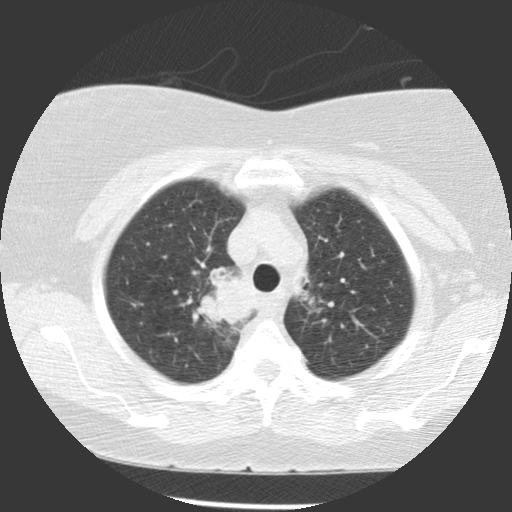
Low-dose screening chest CT, axial slice. First (baseline) screen. Lung window (W 1500 / L -600 HU). 2.5 mm slice thickness. Slice 91 of 116 in the series. 512 × 512 image matrix, field of view 320 × 320 mm. Female participant, aged 63 years at enrolment.
• Expert-annotated lung lesion, box from (x=200, y=266) to (x=258, y=328) px.
• Screening reader's record for this exam (one nodule recorded; not confirmed to be the boxed lesion): non-calcified nodule or mass ≥4 mm, right upper lobe, 39 × 36 mm, spiculated (stellate) margins, soft tissue attenuation.
• Official screen result: positive, change unspecified: nodule(s) >= 4 mm or enlarging nodule(s), mass(es), or other non-specific abnormalities suspicious for lung cancer.
• Lung cancer was diagnosed 72 days after this screen: non-small cell carcinoma, right upper lobe, carina, right main stem bronchus, poorly differentiated (G3), stage IIIA (AJCC 6th edition), 66 mm at pathology.